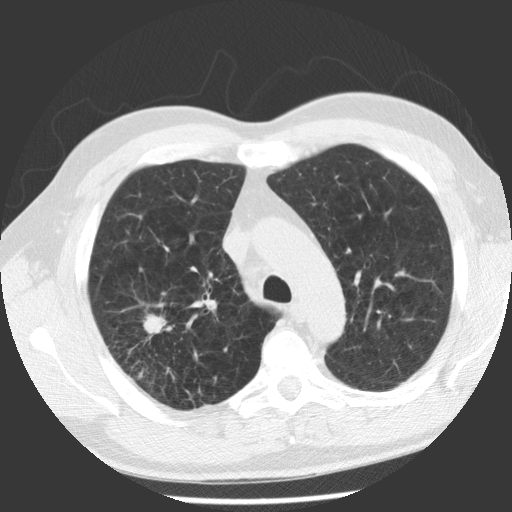
Axial slice from a low-dose chest CT screening exam; baseline screening round; lung window (W 1500 / L -600 HU); standard (soft-tissue) reconstruction kernel (STANDARD); 140 kVp; slice 83 of 112 in the series. Male participant, aged 62 years at enrolment.
Expert-annotated lung lesion, box from (x=114, y=301) to (x=191, y=377) px. The screening reader recorded 2 non-calcified nodules or masses ≥4 mm on this exam (right upper lobe, right upper lobe); which of them this box marks is not recorded. Official screen result: positive, change unspecified: nodule(s) >= 4 mm or enlarging nodule(s), mass(es), or other non-specific abnormalities suspicious for lung cancer. Lung cancer was diagnosed 71 days after this screen: adenocarcinoma, NOS, right upper lobe, poorly differentiated (G3), stage IV (AJCC 6th edition), 30 mm at pathology.